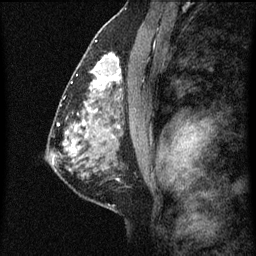
Breast MRI (dynamic contrast-enhanced), one sagittal slice. Dynamic contrast-enhanced series, image 2 of 7 at this slice position (ordered by acquisition). 1.5 T. TE 4.2 ms, TR 8 ms. 2 mm slice thickness. 256 × 256 image matrix. Female patient, age 51 years.
Structures marked on this image (semi-automatic segmentation, software-assisted and operator-edited):
- analysis volume of interest (the breast-tissue region the enhancement analysis was run in; not a lesion): bounding box [x1, y1, x2, y2] px = [86, 48, 125, 101]
- tumour enhancement mask (voxels above the 70 % enhancement threshold inside the analysis volume of interest): [91, 56, 122, 93]